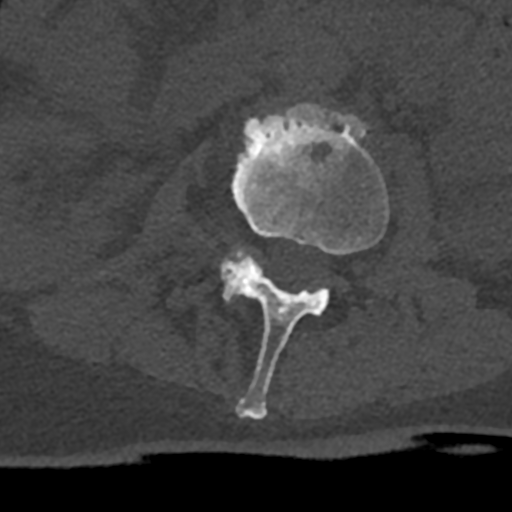
CT including the spine, one axial slice; slice 365 of 797 in the series (ordered by position); reconstruction kernel Br40s/3; 120 kVp; bone window (W 1800 / L 400 HU); 0.5 mm slice thickness; 512 × 512 image matrix, field of view 160 × 160 mm. Patient: male, 74 years. Case-level facts recorded for this patient, not image findings: primary cancer: renal; vertebrae with lytic lesions (as recorded): T10, L1, L2, L3, L4, L5.
Annotated regions visible in this slice (semi-automatically segmented with operator editing):
- L2 vertebra: box from (x=220, y=104) to (x=389, y=420) px
- L3 vertebra: (x=222, y=248)–(x=259, y=300)